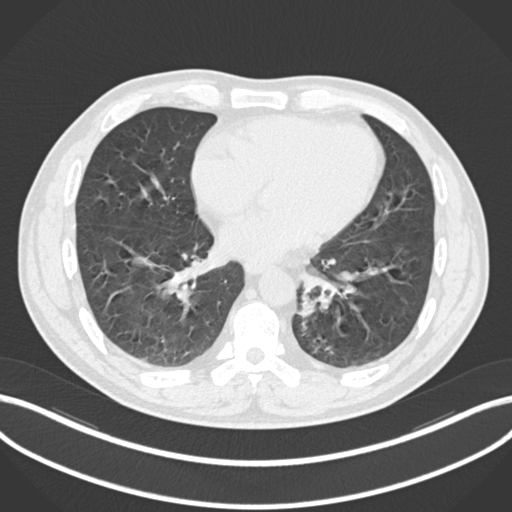
Chest CT, one axial slice. Position 76 of 223 along the scan axis. Reconstruction kernel B30f. 120 kVp. Lung window (W 1500 / L -600 HU). 512 × 512 image matrix, field of view 400 × 400 mm. Patient: male, 50 years. From the clinical record (not read from this slice): clinical TNM (as recorded): T2a N3 M0.
Annotated regions visible in this slice (bounding box drawn by a radiologist):
- lung tumour (recorded histology: squamous cell carcinoma): bounding box (x1, y1, x2, y2) in pixels: (294, 288, 321, 323)